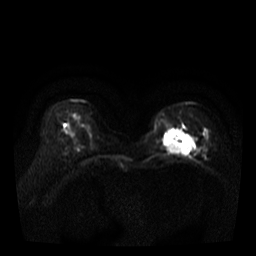
Breast MRI, one axial slice; slice 13 of 35 in the series (ordered by position); diffusion-weighted series; image 2 of 4 stored at this slice position (different b-values; order by instance number); 3 T; 256 × 256 image matrix, field of view 320 × 320 mm. Female patient.
Annotated regions visible in this slice (outlined manually by an expert reader):
- tumour on diffusion-weighted imaging: bounding box [x1, y1, x2, y2] px = [162, 130, 194, 156]